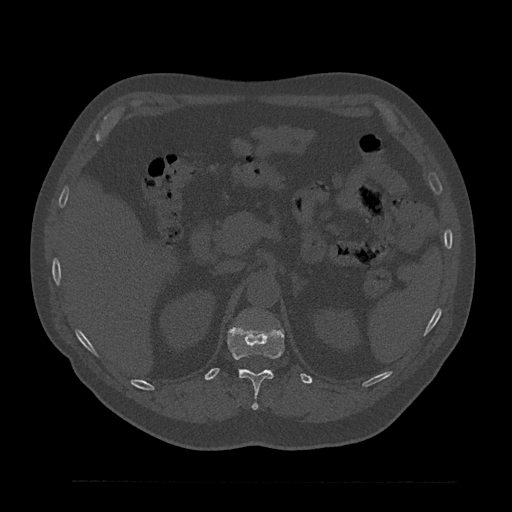
CT including the spine, one axial slice. Slice 219 of 797 in the series (ordered by position). Reconstruction kernel Br40s/3. Bone window (W 1800 / L 400 HU). 0.5 mm slice thickness. 512 × 512 image matrix, field of view 430 × 430 mm. Male patient, age 61 years. Case-level facts recorded for this patient, not image findings: primary cancer: prostate.
Outlined on this slice (semi-automatic segmentation, software-assisted and operator-edited):
- T12 vertebra: bounding box [x1, y1, x2, y2] px = [227, 324, 285, 410]